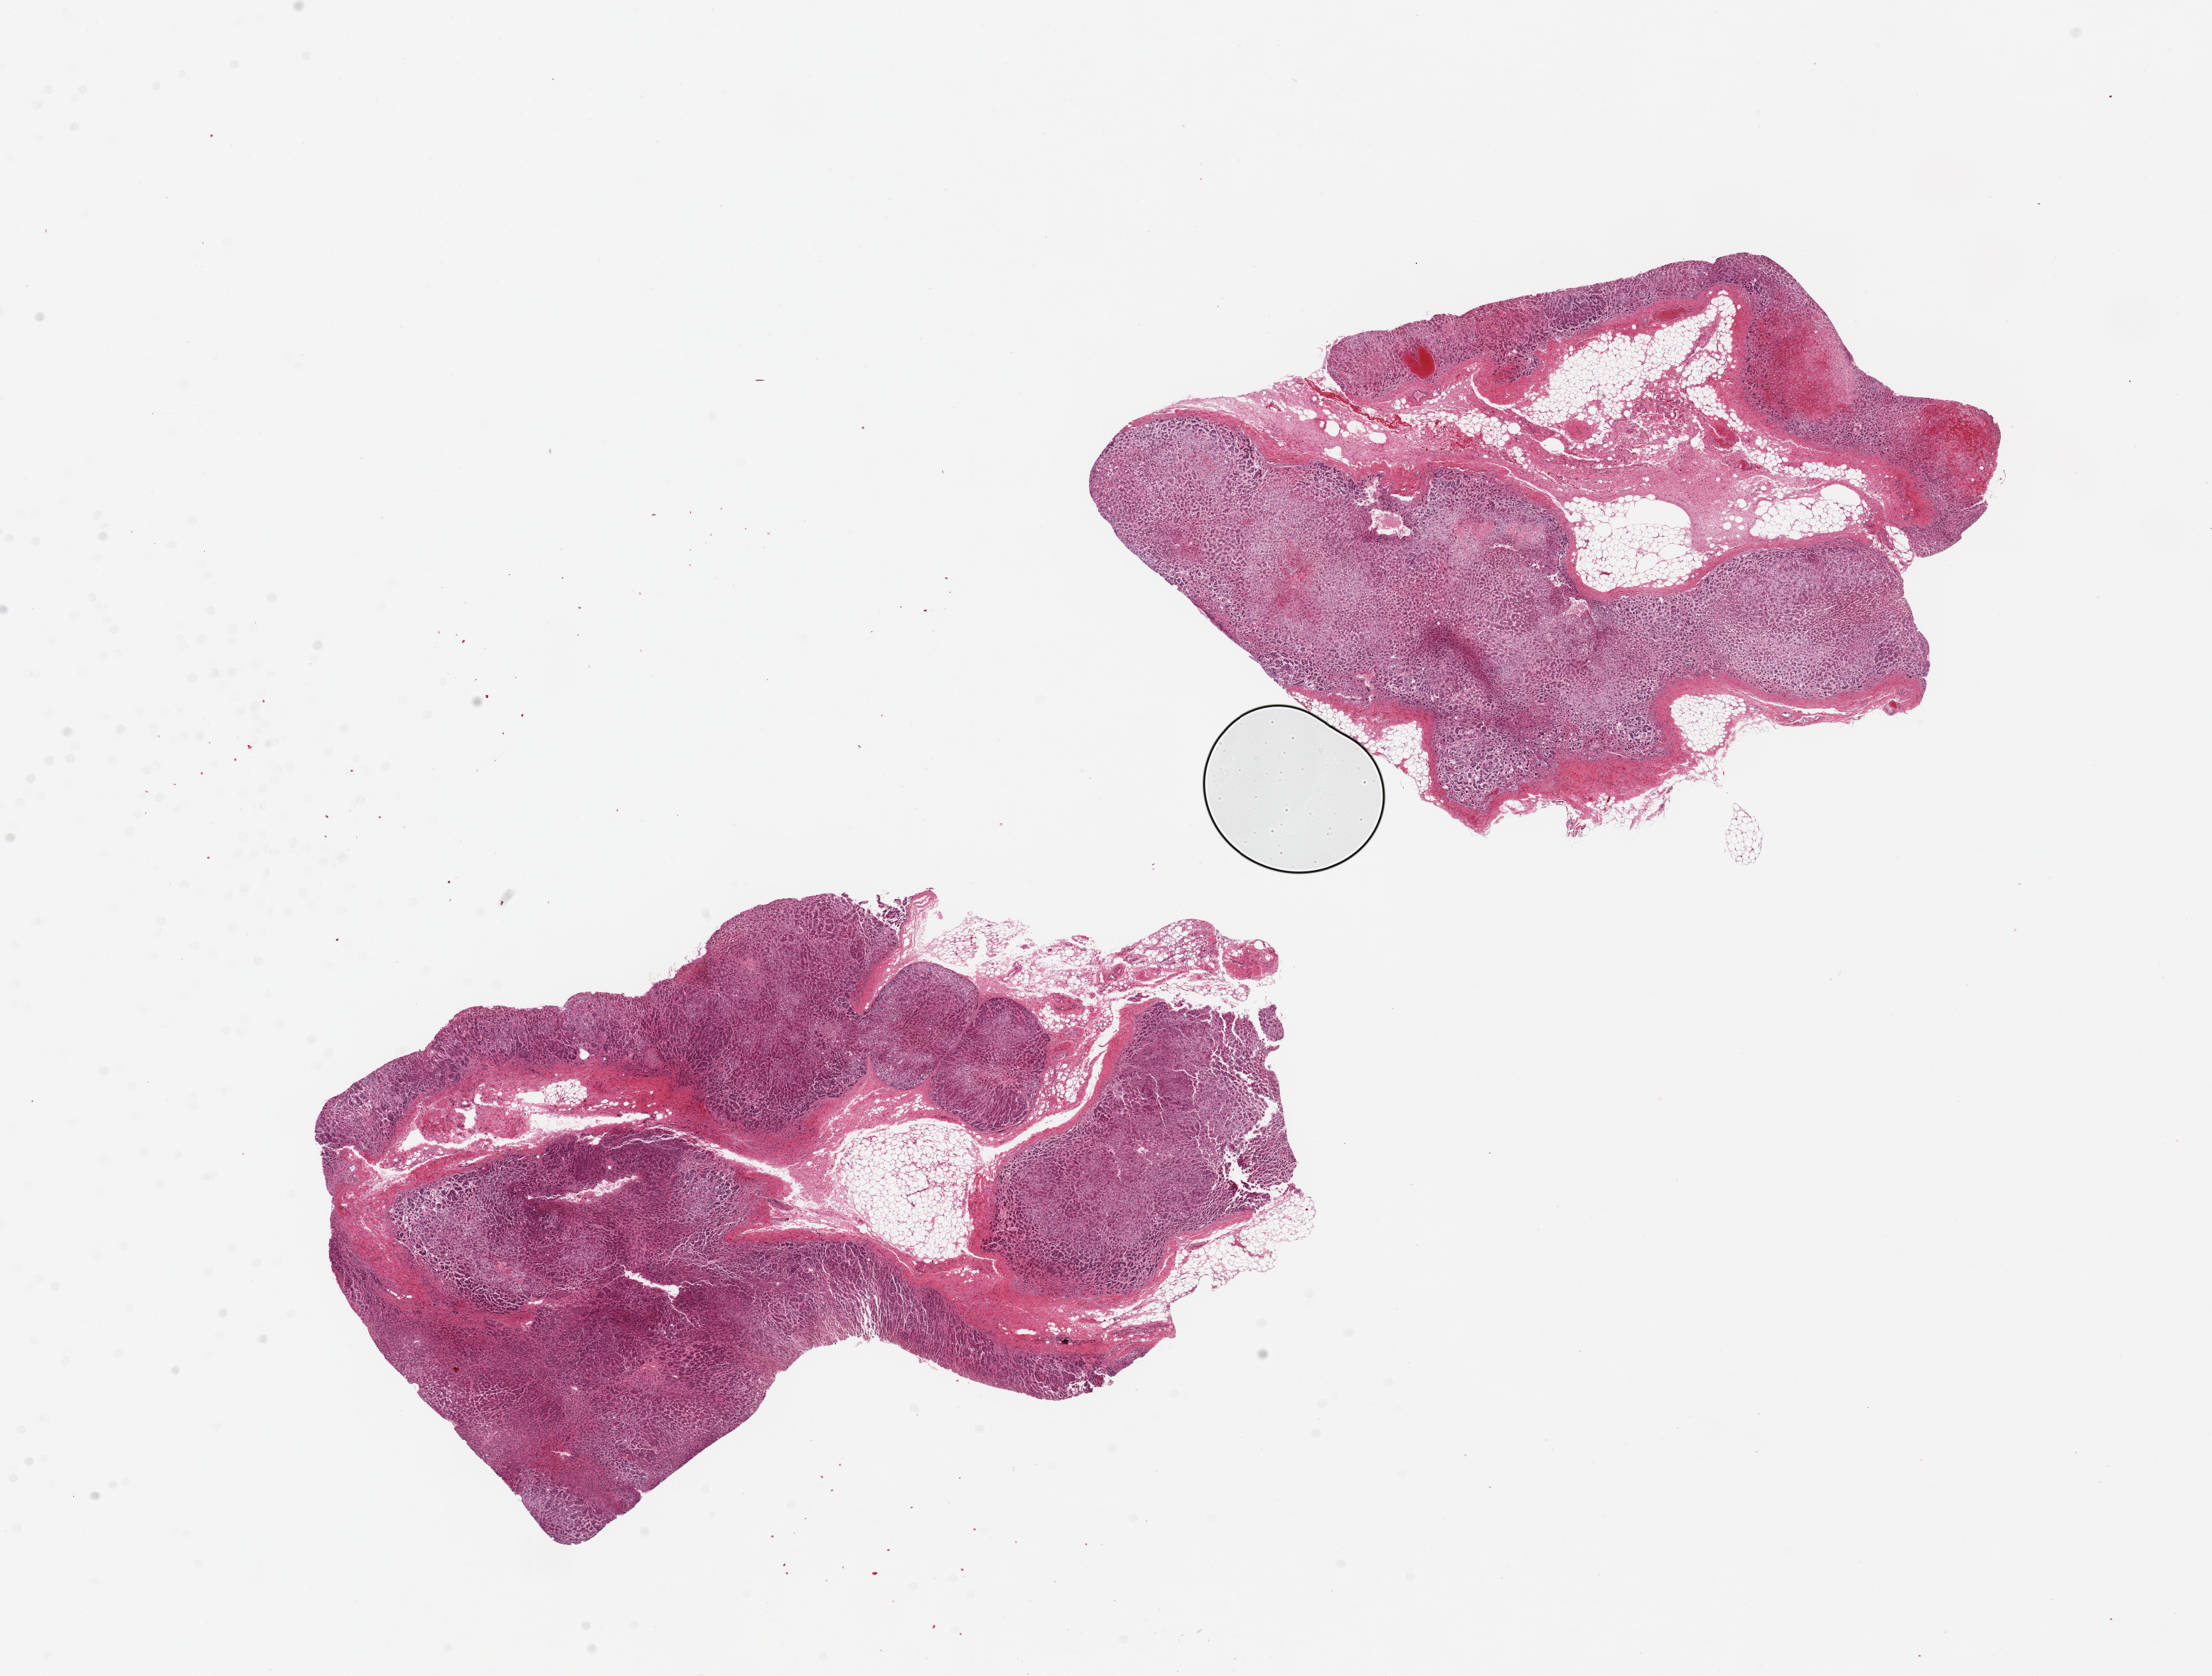
Digitized haematoxylin and eosin-stained section, brightfield, a low-resolution overview of the entire scanned area, about 24.6 x 18.6 mm. PAXgene-fixed paraffin-embedded (PFPE) section. Sampled site (target tissue): adrenal gland. Donor tissue sample.
• reviewer comment on this tissue sample: 2 pieces, 11x6 & 10x7mm; 10 and 20% internal adipose